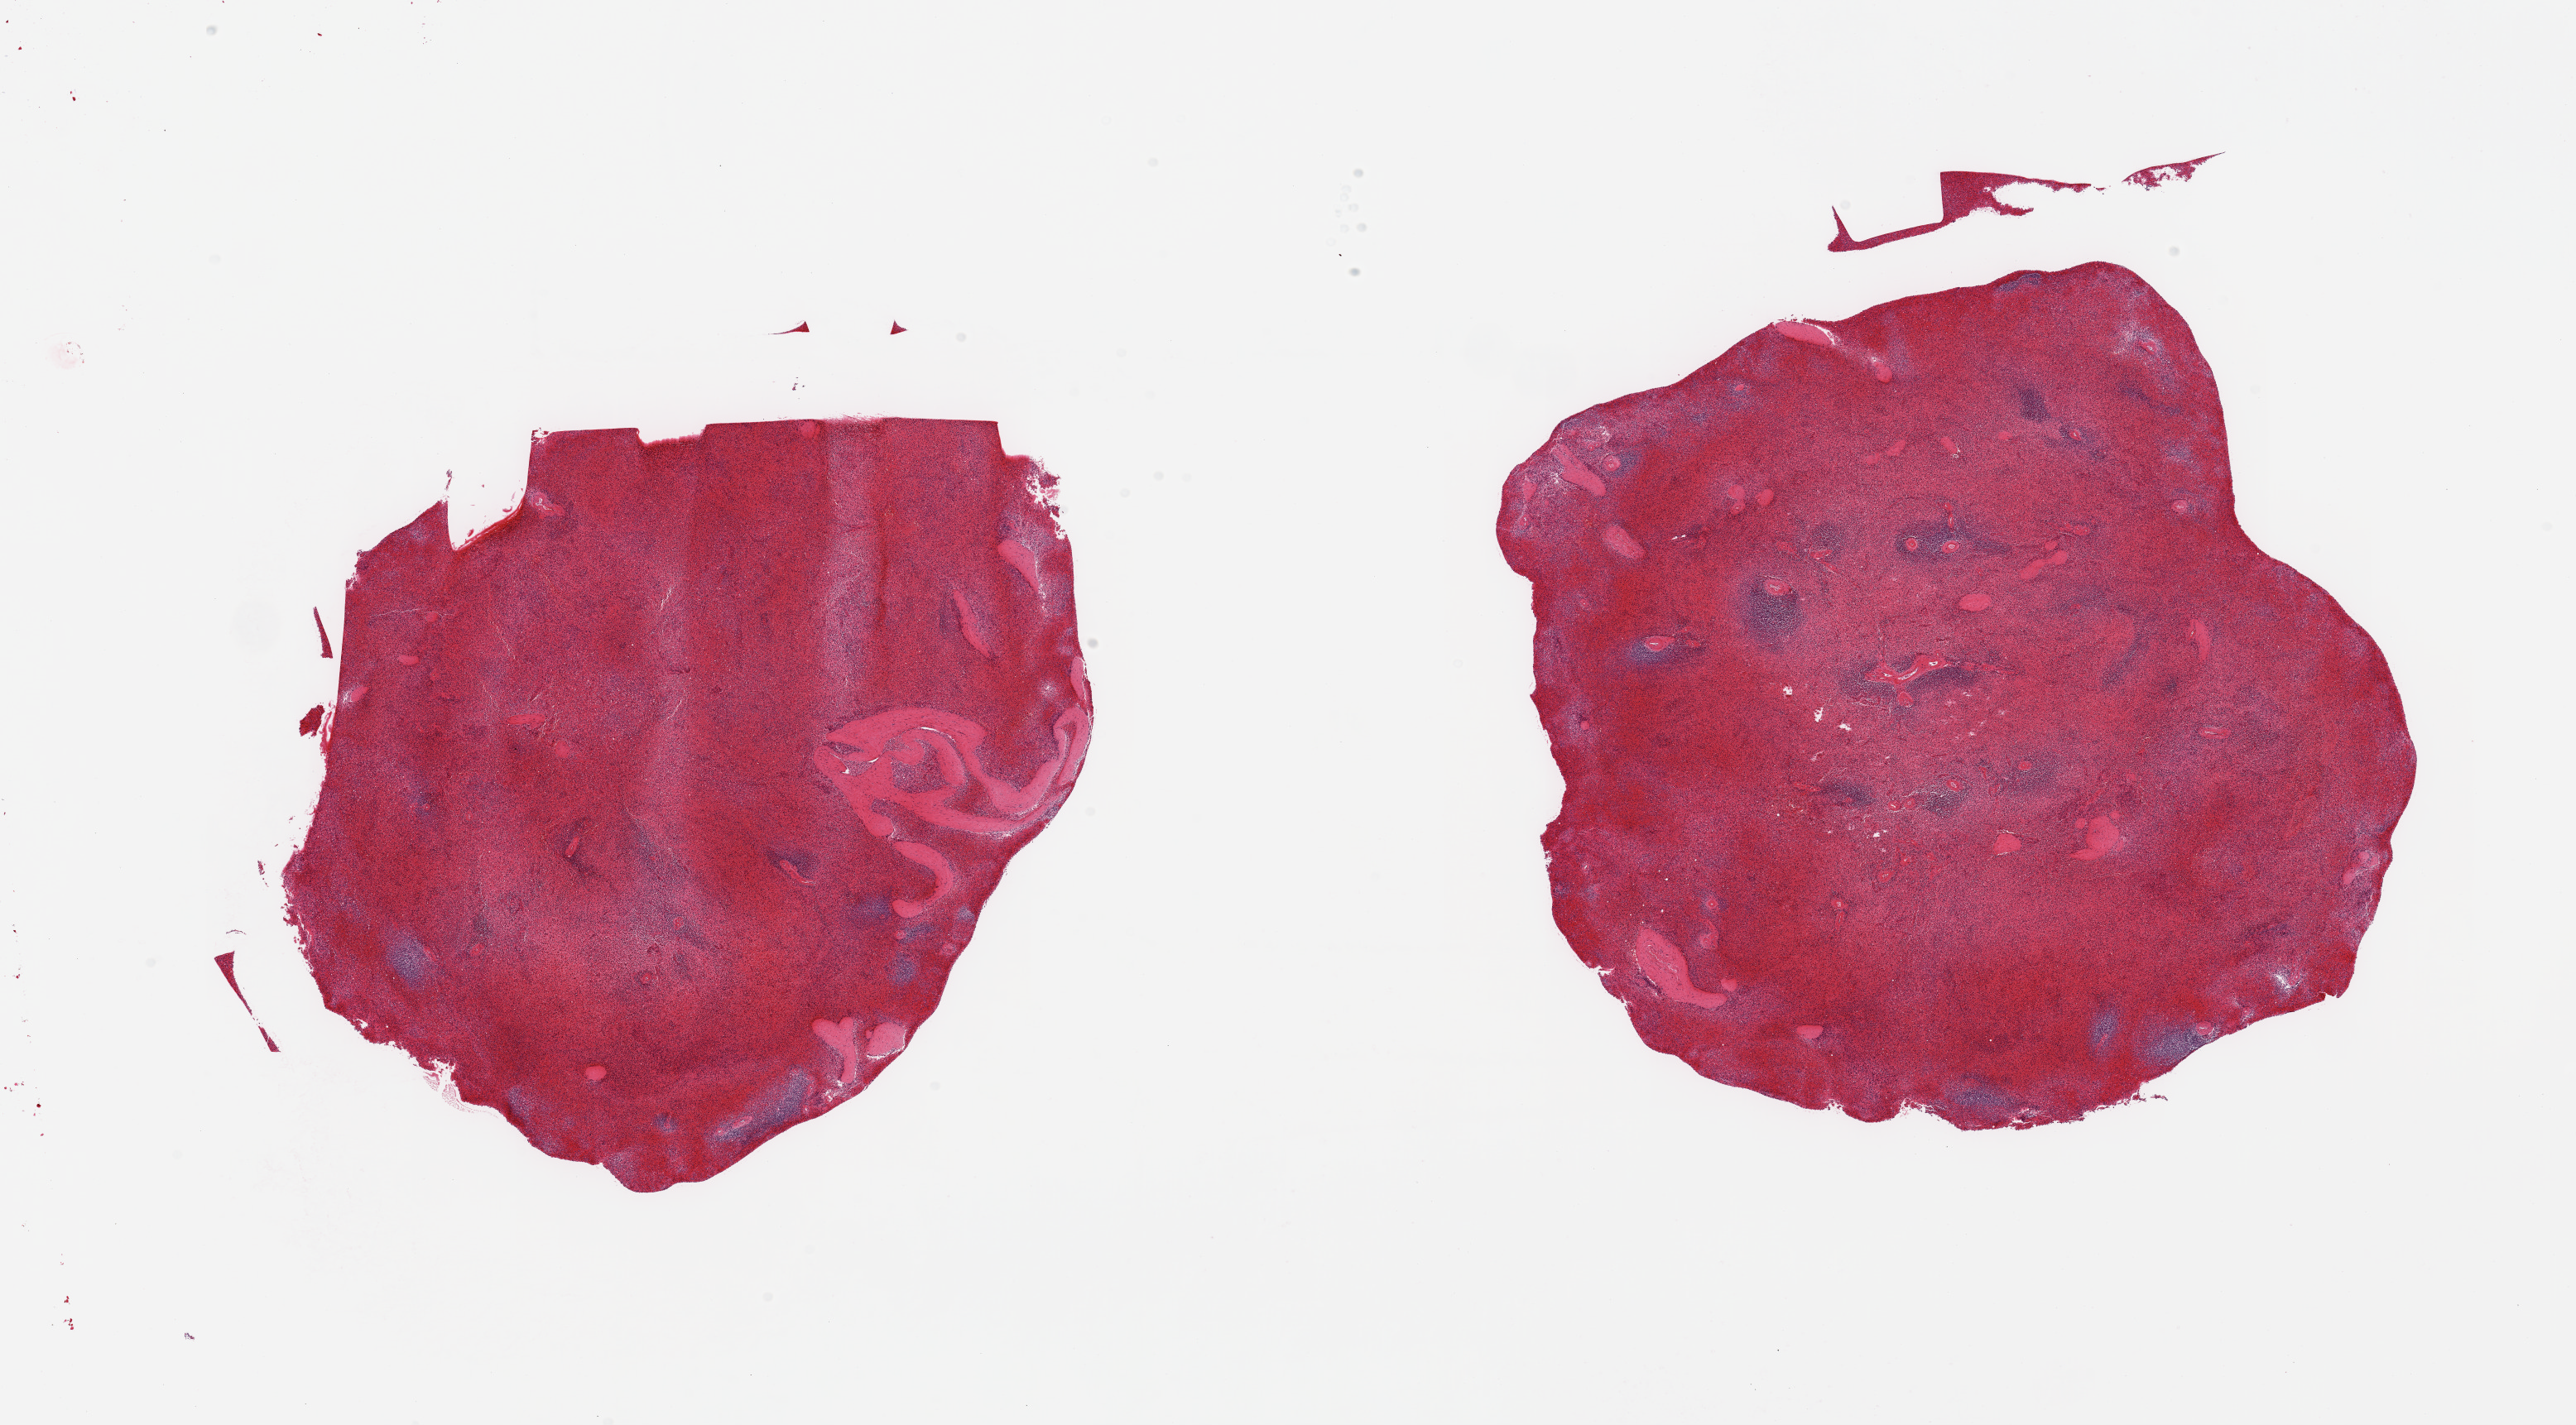
Haematoxylin and eosin whole-slide image, whole scanned area (about 24.6 x 13.6 mm) shown as a low-resolution overview. PAXgene-fixed, paraffin-embedded tissue. Section of spleen (target tissue). Donor tissue sample. Donor: male.
Pathologist's review note for this sample: 2 pieces; moderate congestion.